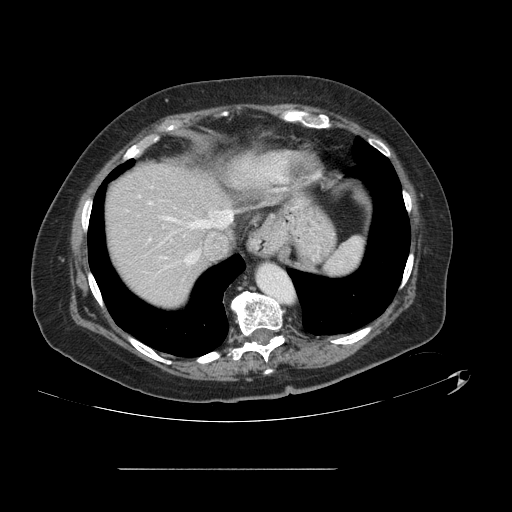
Contrast-enhanced abdominal CT, one axial slice; slice 114 of 148 in the series (ordered by position); intravenous contrast given; soft-tissue window (W 400 / L 40 HU); 2.5 mm slice thickness; 512 × 512 image matrix, field of view 439 × 439 mm. Female patient, age 75 years. From the clinical record (not read from this slice): diagnosis: colorectal cancer liver metastases, imaged before liver resection; multiple liver metastases: no; largest metastasis: 2.4 cm; chemotherapy before resection: no.
Annotated regions visible in this slice (manually delineated by an expert):
- hepatic veins: bounding box <166,210,233,264> (left, top, right, bottom; pixels)
- liver: <105,165,232,309>
- planned liver remnant (the part of the liver to remain after resection): <105,165,233,309>